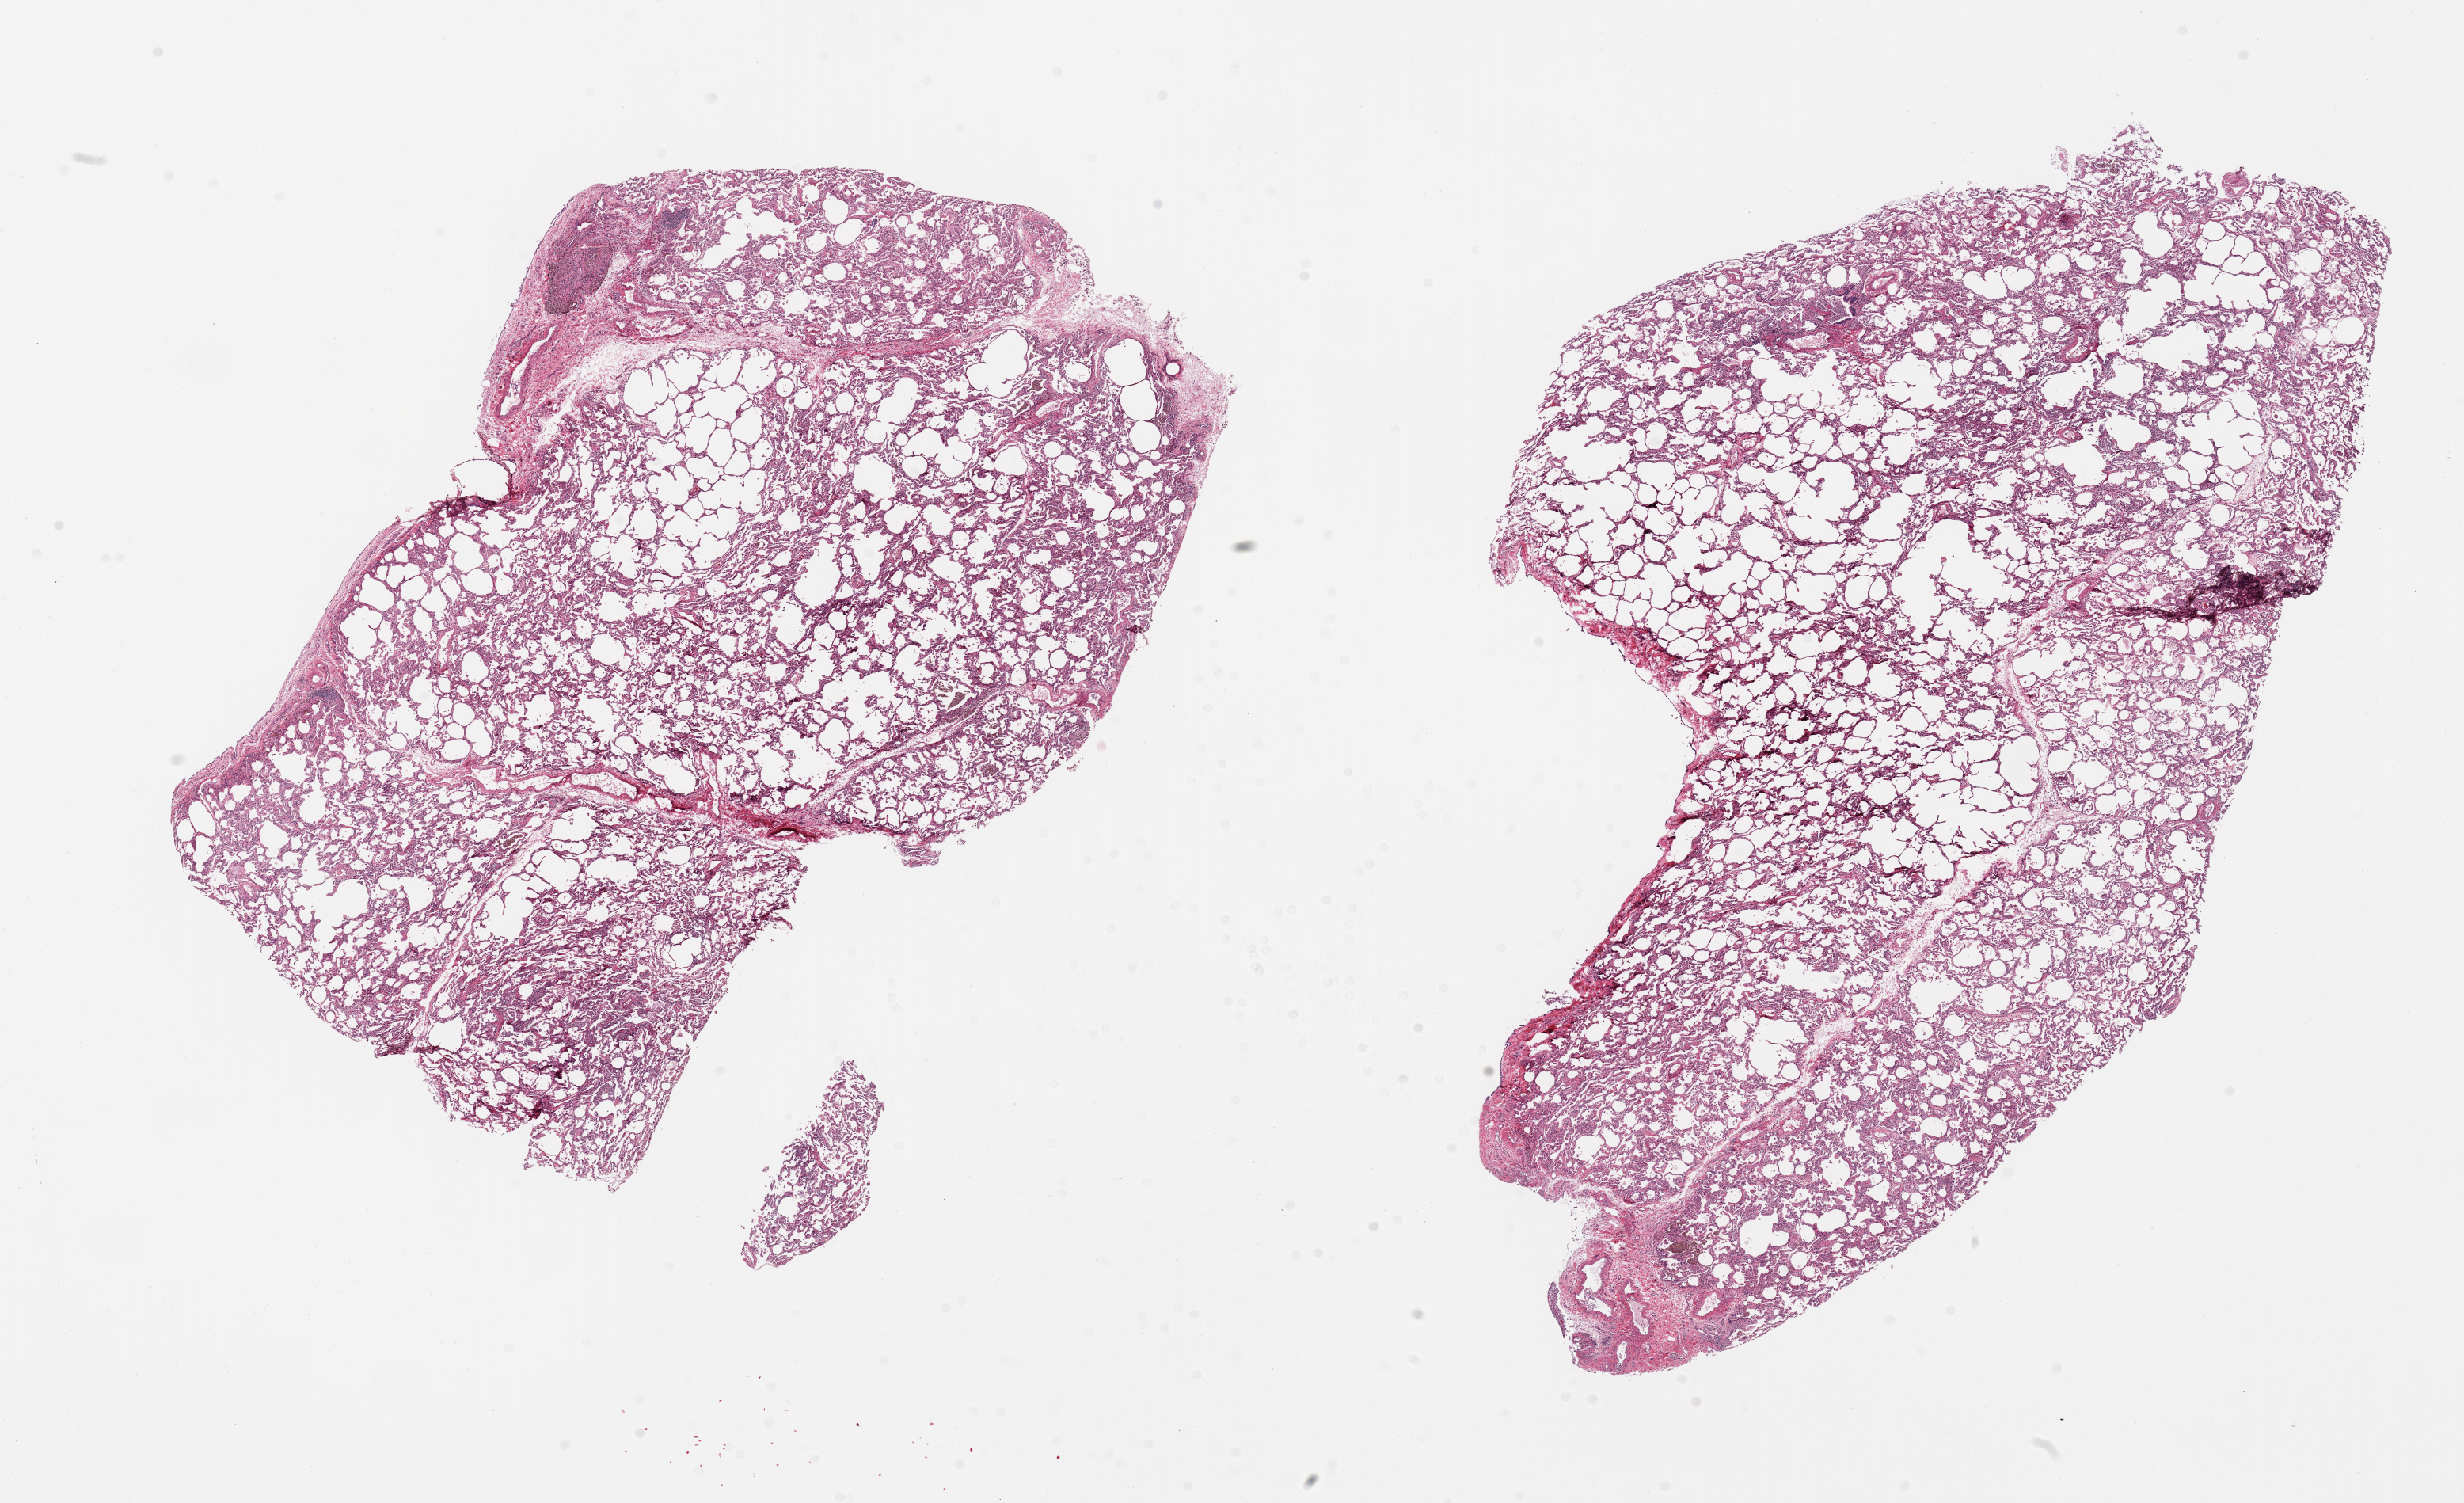
H&E whole-slide image, a low-resolution overview of the entire scanned area, about 24.6 x 15.0 mm (slide scanned at 20x). PAXgene-fixed paraffin-embedded (PFPE) section. Sampled site (target tissue): lung. Donor tissue sample. Donor sex: female.
Pathologist's review note for this sample: 2 pieces; scattered foci of bronchopneumonia; mild emphysema; pigmented macrophages in alveoli and lymph nodule.